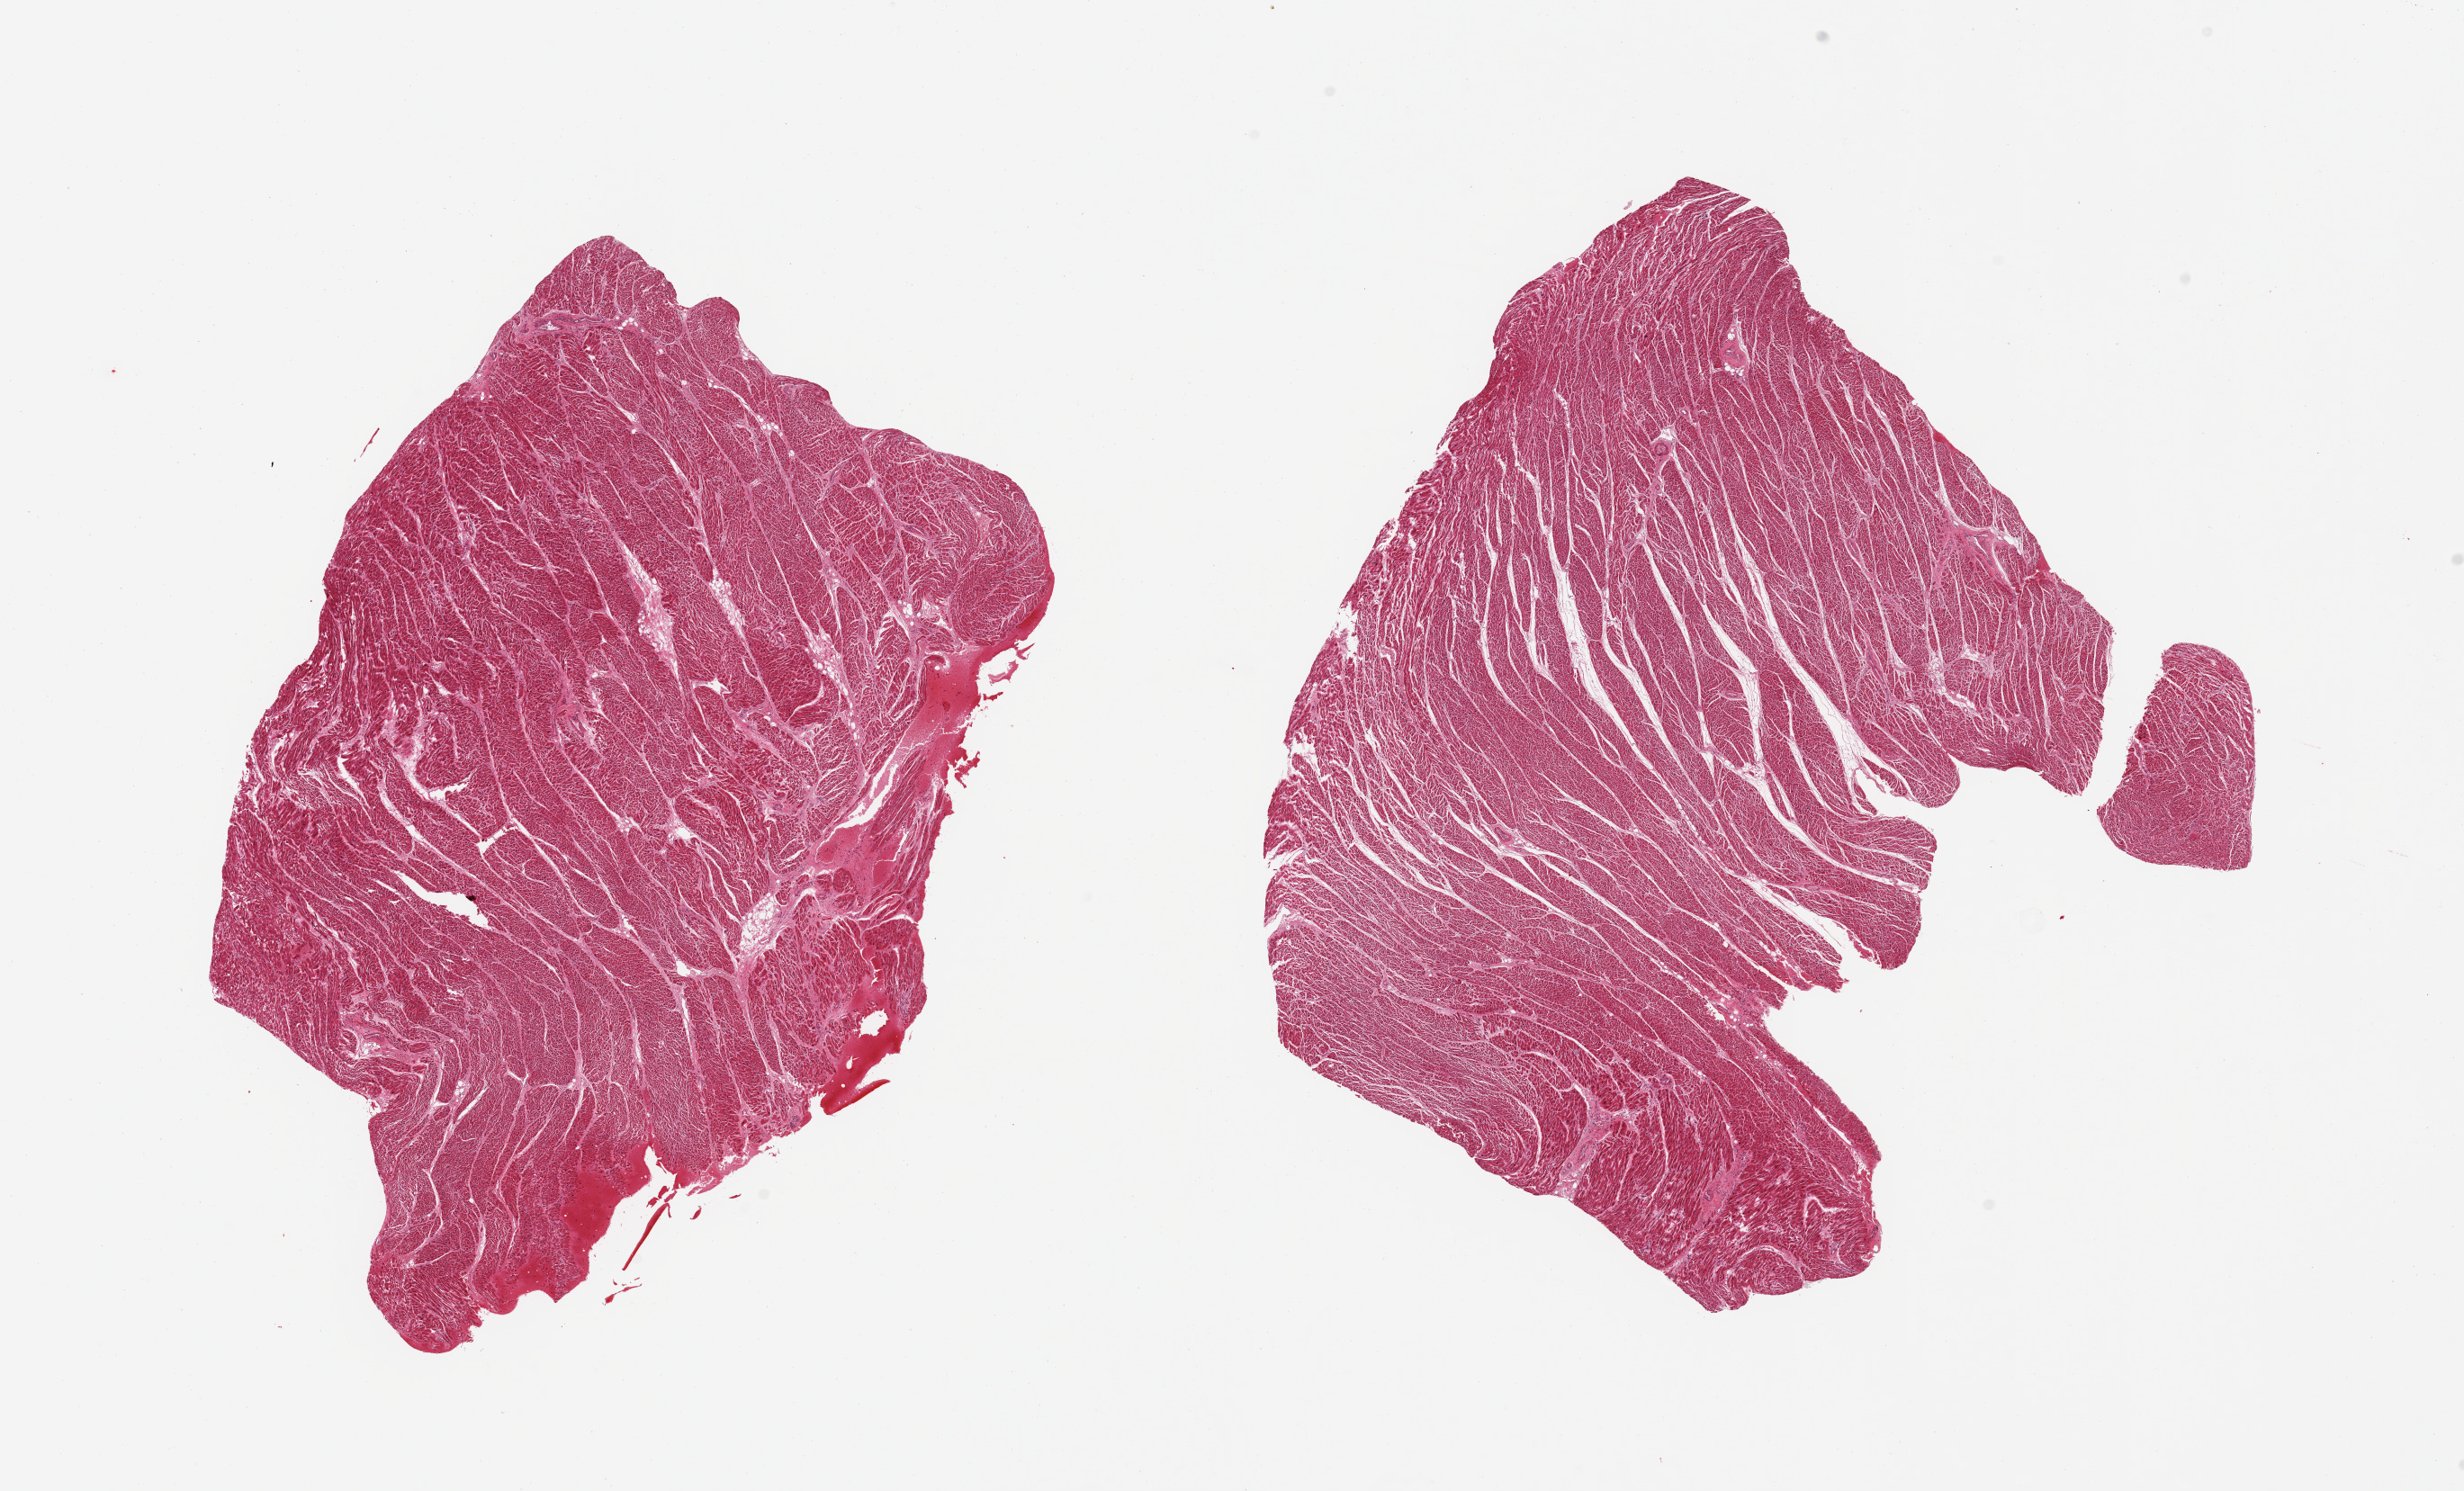
Hematoxylin and eosin (H&E) whole-slide image, a low-resolution overview of the entire scanned area, about 21.7 x 13.1 mm (slide scanned at 20x). PAXgene-fixed paraffin-embedded (PFPE) section. Section of heart (target tissue). Donor tissue sample. Male donor.
Pathologist's review note for this sample: 2 pieces, mild interstitial fibrosis/chronic ischemic changes.